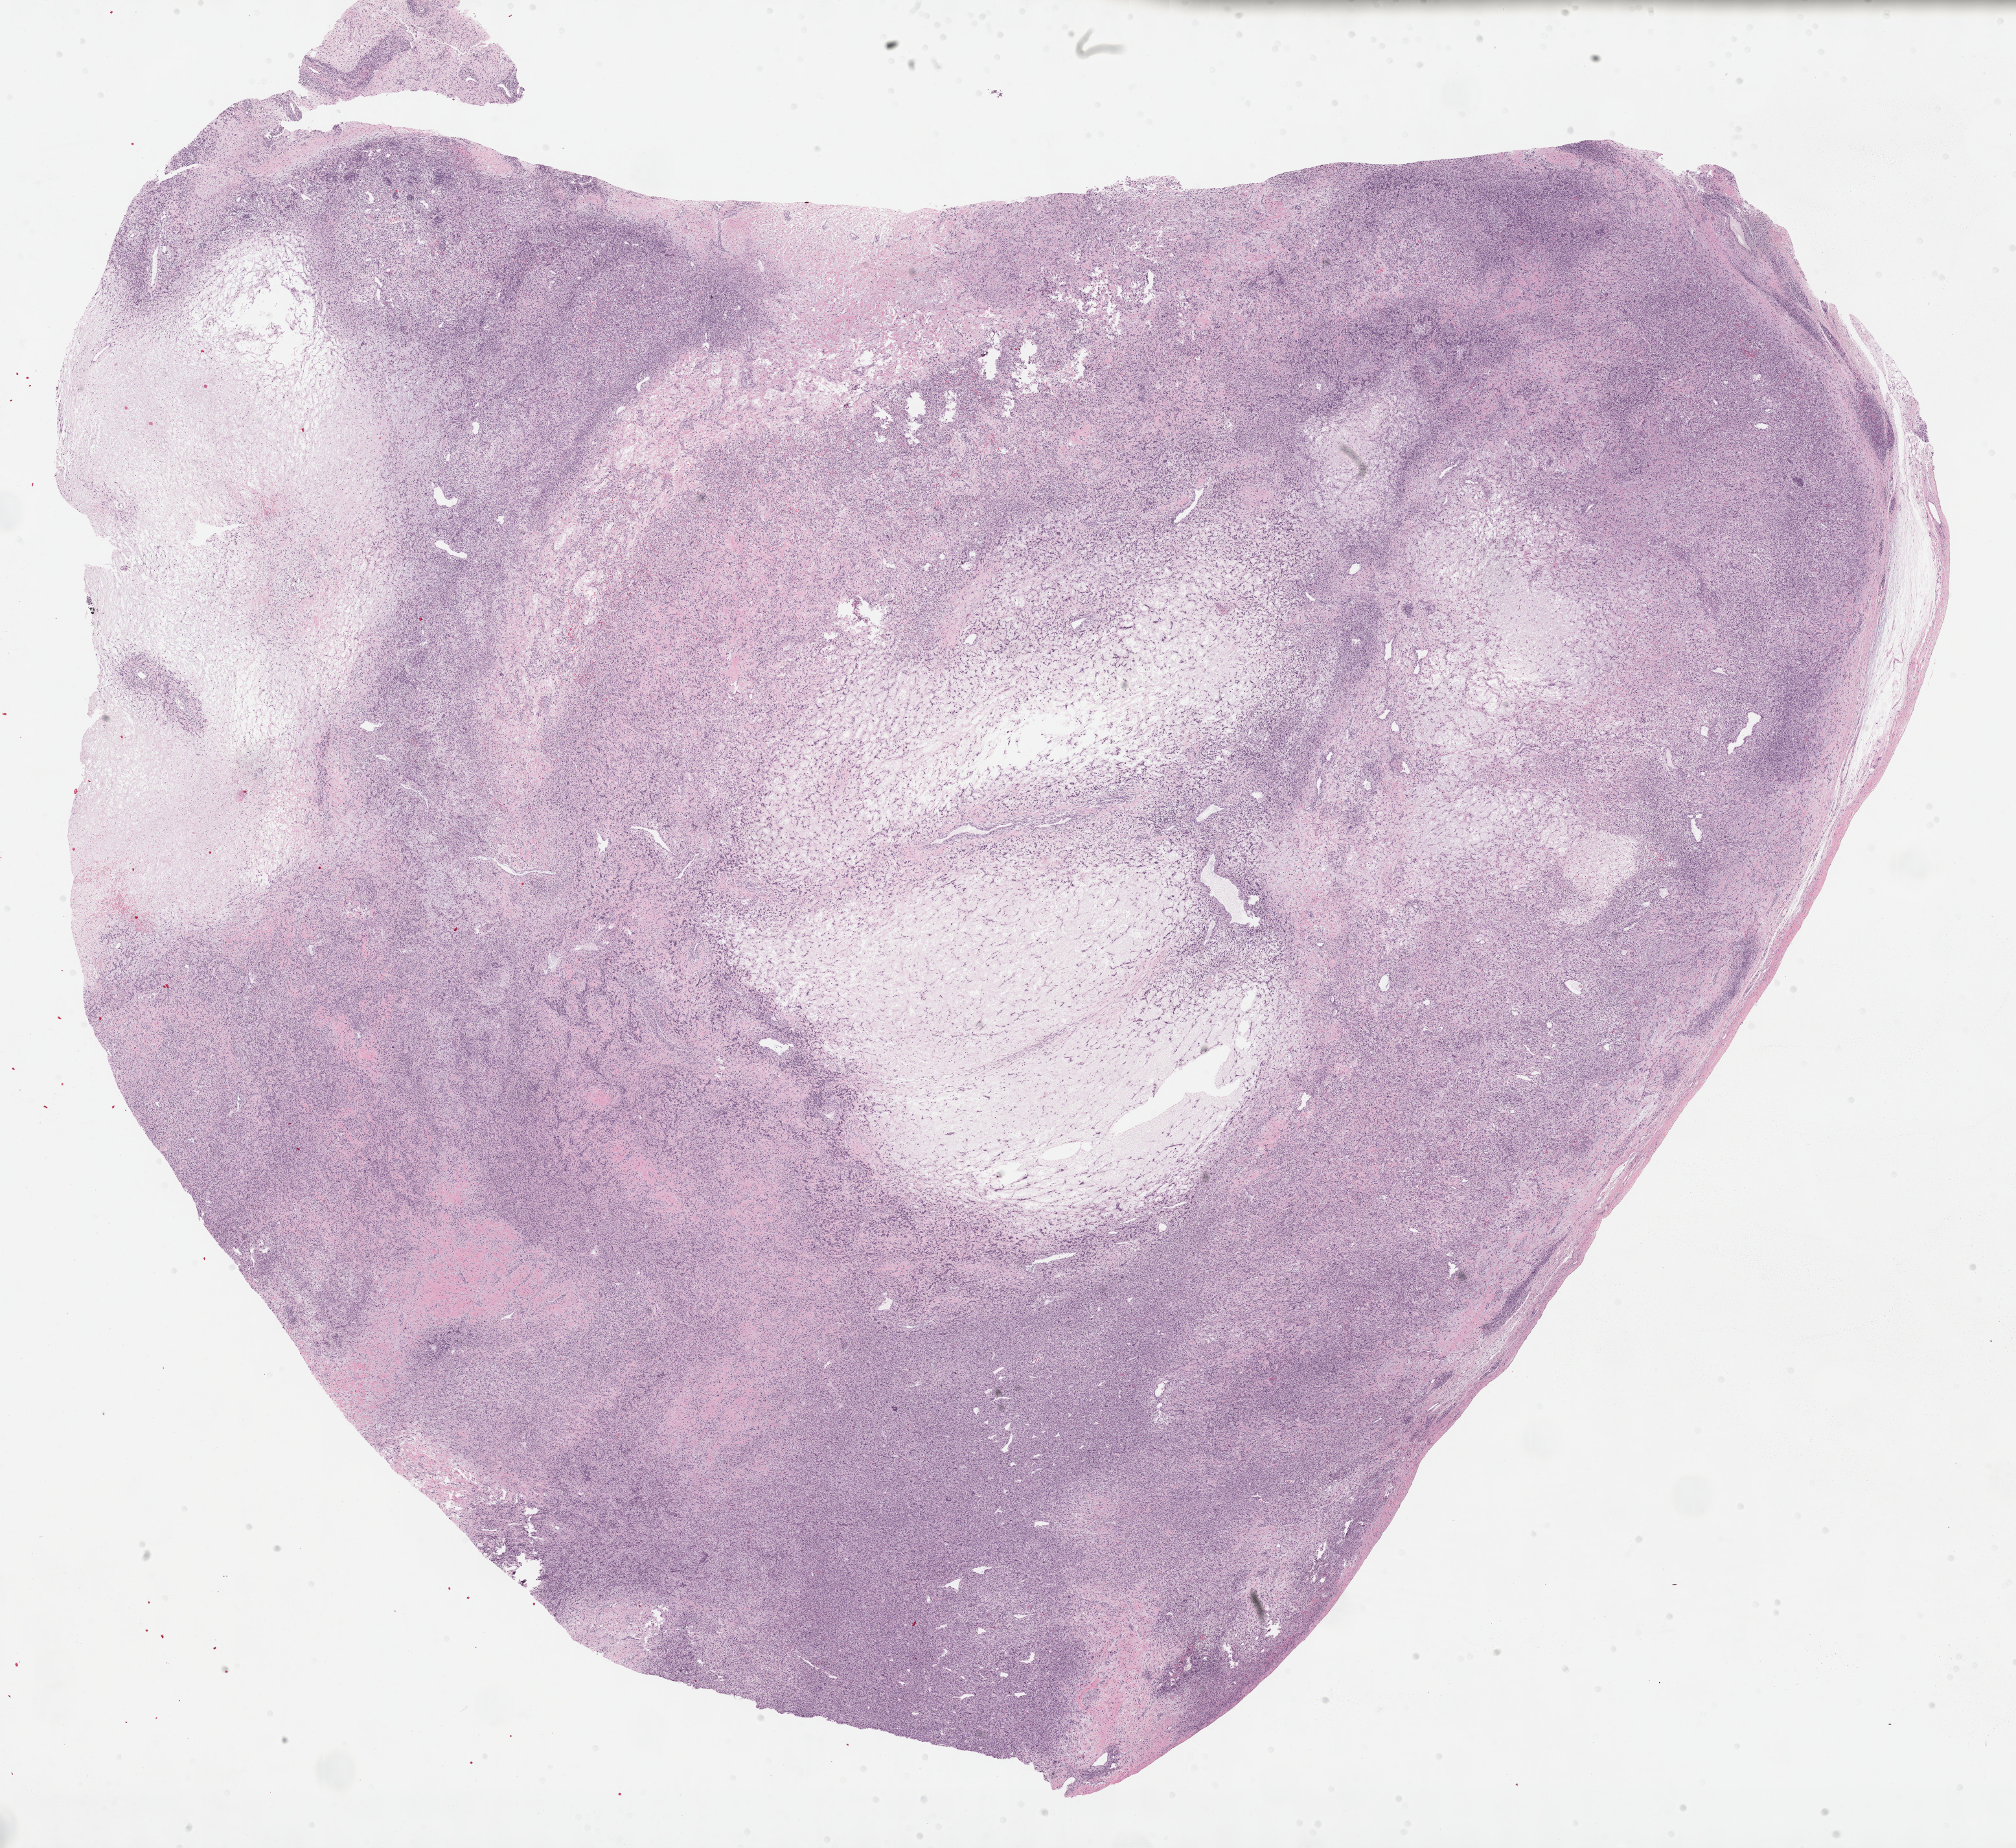
Digitized H&E tissue section (whole slide), whole scanned area (about 25.2 x 23.1 mm) shown as a low-resolution overview, formalin-fixed paraffin-embedded (FFPE) diagnostic section, primary tumour sample from the retroperitoneum and peritoneum. Female patient; age at initial diagnosis 80 years.
Pathologic diagnosis: Dedifferentiated liposarcoma (retroperitoneum).